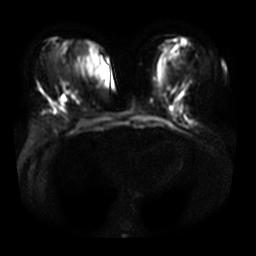
Breast MRI, one axial slice. Position 12 of 33 along the scan axis. Diffusion-weighted series; image 2 of 4 stored at this slice position (different b-values; order by instance number). 3 T. 256 × 256 image matrix. Female patient.
Structures marked on this image (expert manual segmentation):
- tumour on diffusion-weighted imaging: bounding box <60,81,66,87> (left, top, right, bottom; pixels)